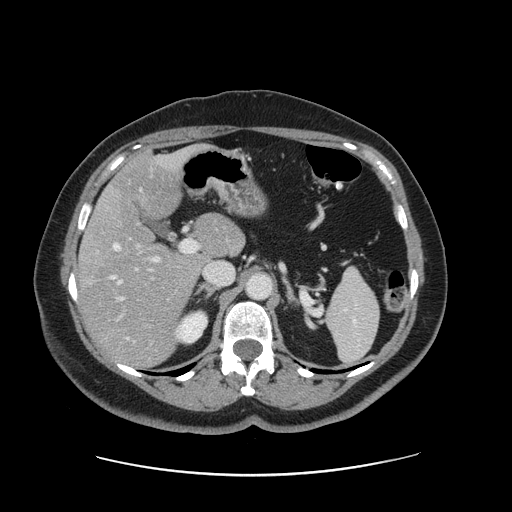
Contrast-enhanced abdominal CT, one axial slice; position 86 of 161 along the scan axis; intravenous contrast given; soft-tissue window (W 400 / L 40 HU); 2.5 mm slice thickness; 512 × 512 image matrix, field of view 398 × 398 mm. Female patient, age 62 years. Case-level facts recorded for this patient, not image findings: diagnosis: colorectal cancer liver metastases, imaged before liver resection; multiple liver metastases: no; largest metastasis: 2.5 cm; disease in both lobes: no.
Outlined on this slice (outlined manually by an expert reader):
- hepatic veins: box from (x=111, y=189) to (x=142, y=284) px
- liver: (x=80, y=151)–(x=242, y=367)
- planned liver remnant (the part of the liver to remain after resection): (x=110, y=151)–(x=242, y=262)
- portal vein (with intrahepatic branches): (x=116, y=239)–(x=198, y=321)